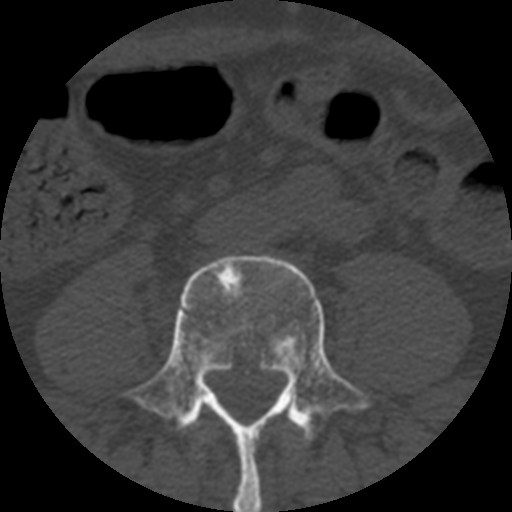
CT including the spine, one axial slice. Slice 94 of 508 in the series (ordered by position). Bone window (W 1800 / L 400 HU). 1.25 mm slice thickness. 512 × 512 image matrix, field of view 160 × 160 mm. Patient age 57 years. Case-level facts recorded for this patient, not image findings: primary cancer: prostate.
Structures marked on this image (semi-automatic segmentation, software-assisted and operator-edited):
- L3 vertebra: bounding box <200,432,205,442> (left, top, right, bottom; pixels)
- L4 vertebra: <123,255,370,512>